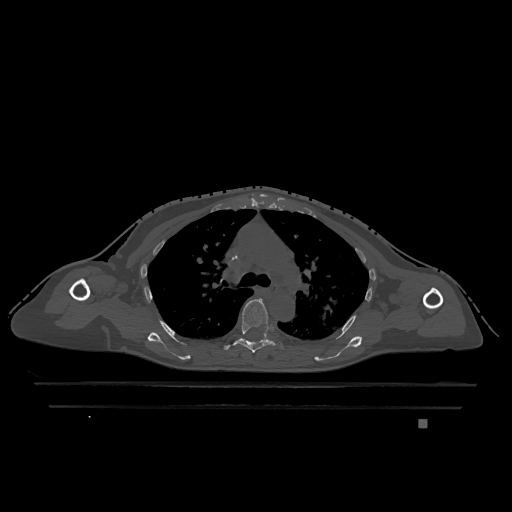
CT including the spine, one axial slice. Position 838 of 1317 along the scan axis. Bone window (W 1800 / L 400 HU). 0.5 mm slice thickness. 512 × 512 image matrix. Patient: female, 74 years. From the clinical record (not read from this slice): primary cancer: lung; vertebrae with lytic lesions (as recorded): T1, T4, T5, T6, L4, L5.
Outlined on this slice (semi-automatically segmented with operator editing):
- T5 vertebra: box from (x=224, y=299) to (x=276, y=353) px